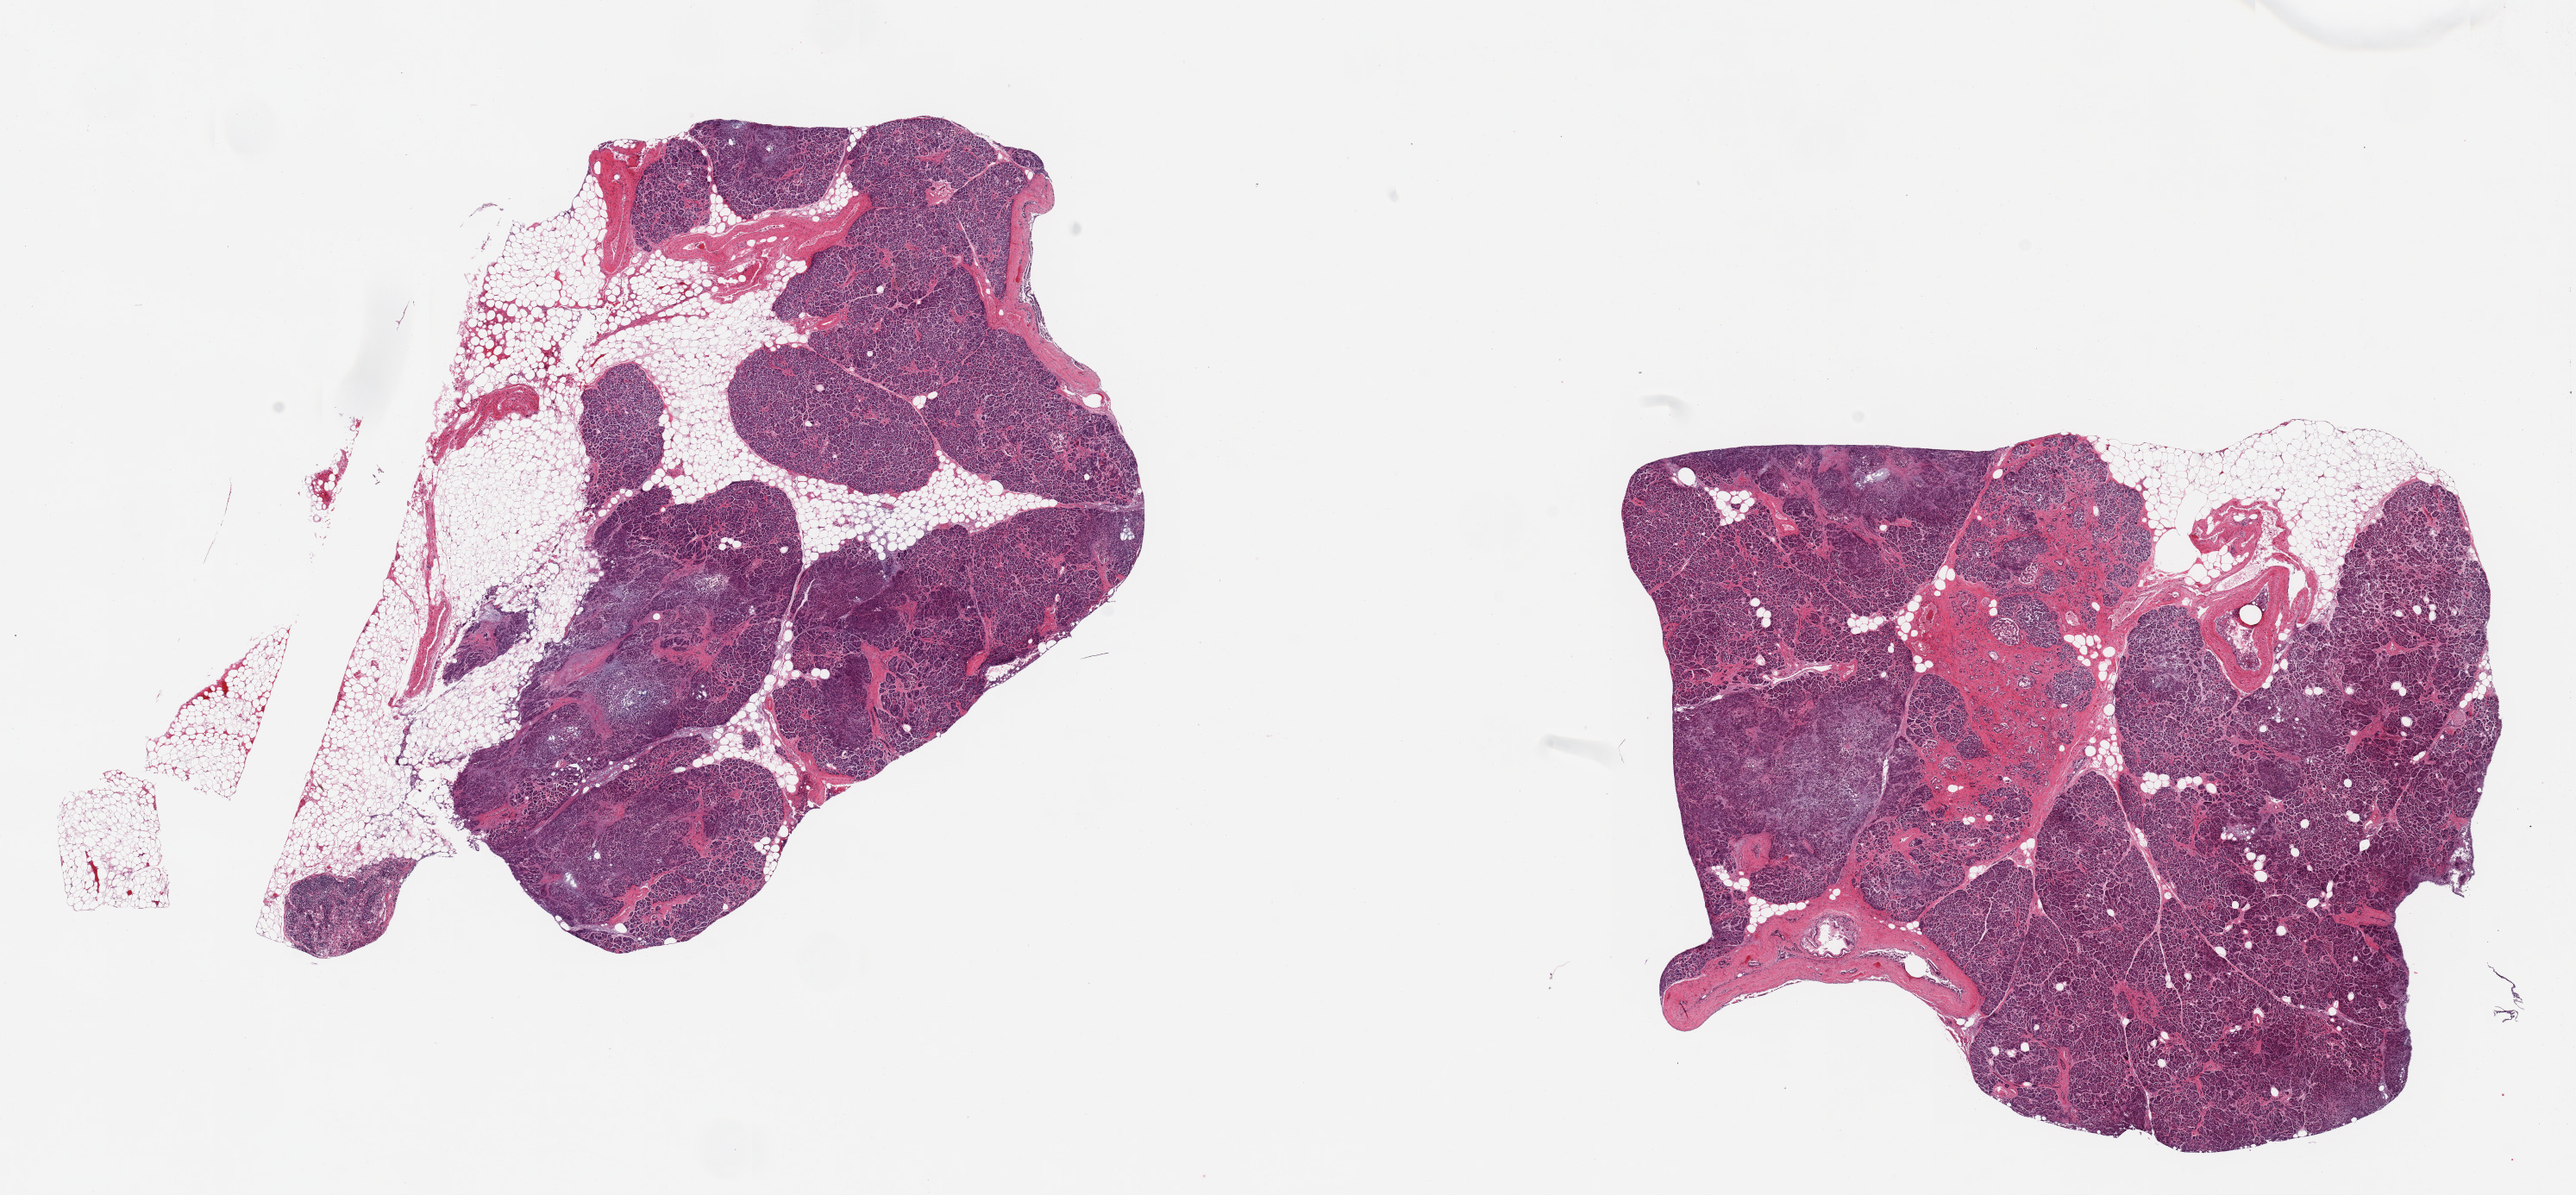
Digitized haematoxylin and eosin-stained section — a low-resolution overview of the entire scanned area, about 23.6 x 11.0 mm; PAXgene-fixed, paraffin-embedded tissue; target tissue: pancreas; donor tissue sample. Donor sex: male.
Reviewer comment on this tissue sample: 2 pieces, modeate-focally severe autolysis/saponification; A few Islets, badly degenerated, visible; Adherent fat is ~20% of specimen.